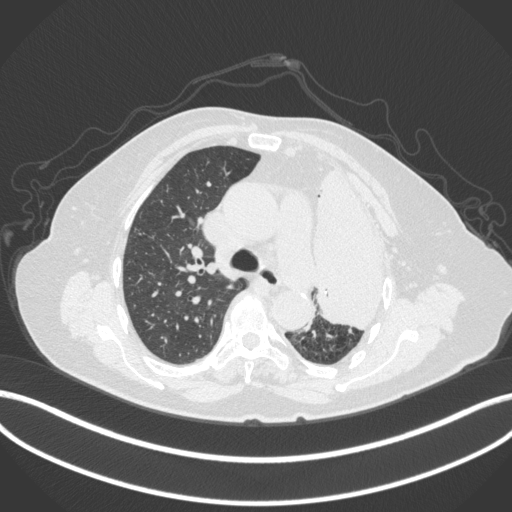
Chest CT, one axial slice; position 265 of 399 along the scan axis; reconstruction kernel B31f; lung window (W 1500 / L -600 HU); 1 mm slice thickness; 512 × 512 image matrix, field of view 400 × 400 mm. Female patient, age 75 years. Case-level facts recorded for this patient, not image findings: clinical TNM (as recorded): T3 N3 M1.
Outlined on this slice (rectangle marked by the reading radiologist):
- lung tumour (recorded histology: adenocarcinoma): bounding box (x1, y1, x2, y2) in pixels: (305, 161, 394, 331)